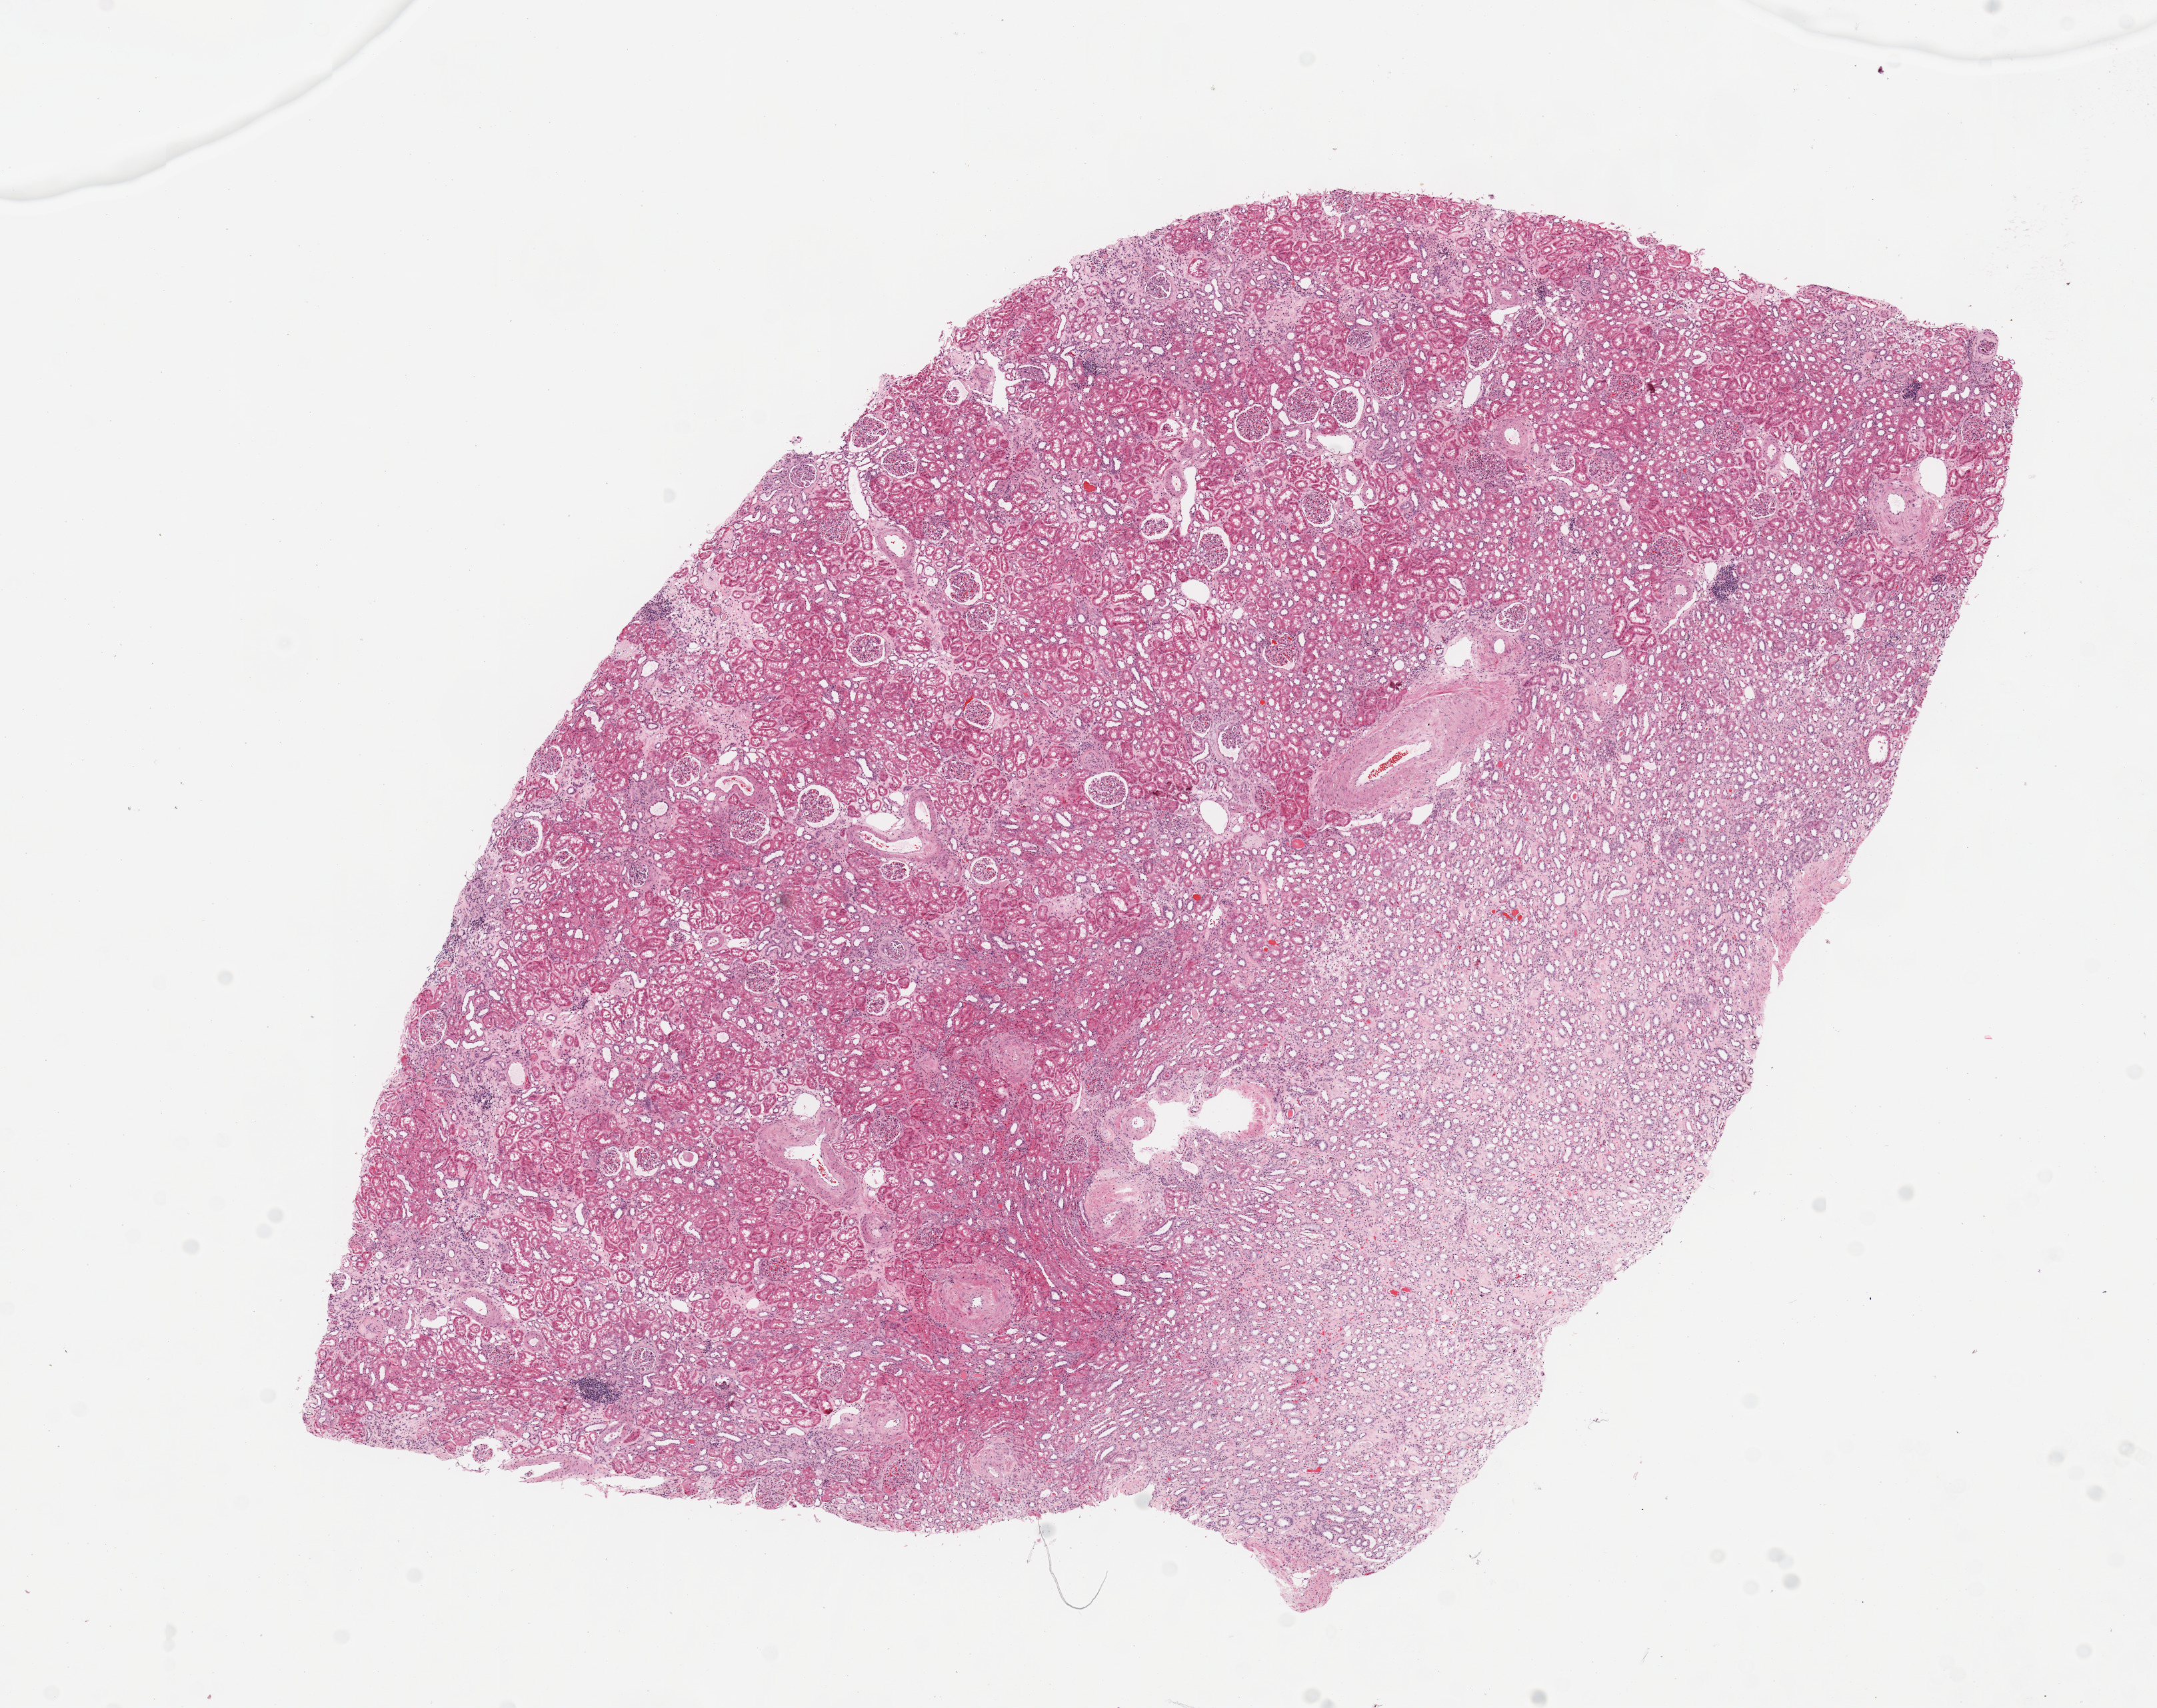
Digitized H&E-stained tissue section (whole slide) — a low-resolution overview of the entire scanned area, about 12.8 x 10.1 mm (from a 20x scan), normal (non-tumour) tissue sample, sampled site: kidney. 72-year-old male patient.
This section: normal (non-tumour) tissue from the same patient. Patient diagnosis: Renal cell carcinoma, NOS.